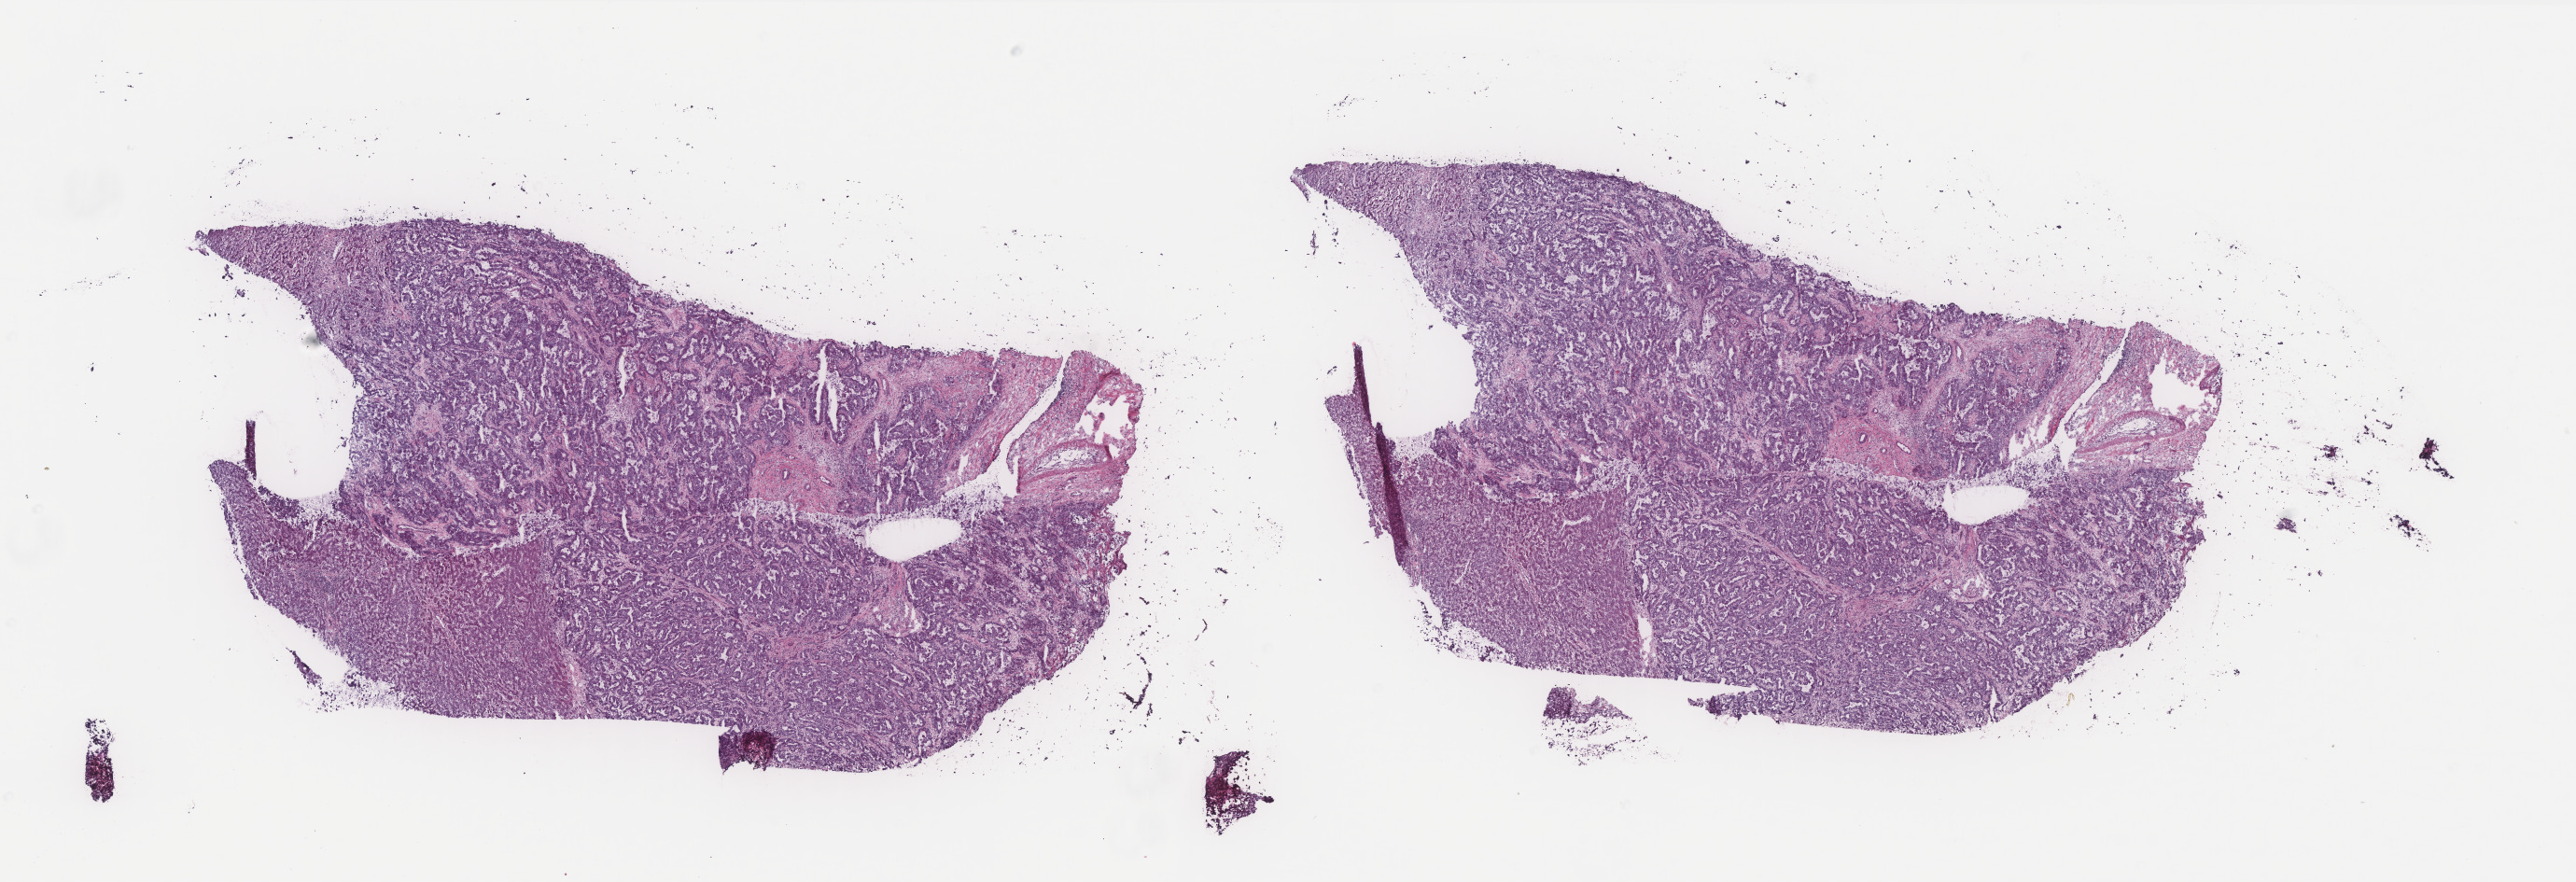
Hematoxylin and eosin (H&E) stained whole-slide image — low-resolution overview of the scanned area, about 22.1 x 7.6 mm (from a 40x scan). Frozen section. Primary tumour sample from the liver. Patient: male, age at initial diagnosis 80 years. Histologic grade: G2 (moderately differentiated). Composition of this section per pathologist review: tumour cells 80%, tumour nuclei 60%, normal cells 15%, stromal cells 5%, necrosis 0%. Infiltration values recorded for this section: lymphocyte infiltration 0%, monocyte infiltration 0%, neutrophil infiltration 0%.
Pathologic diagnosis: Hepatocellular carcinoma, NOS.